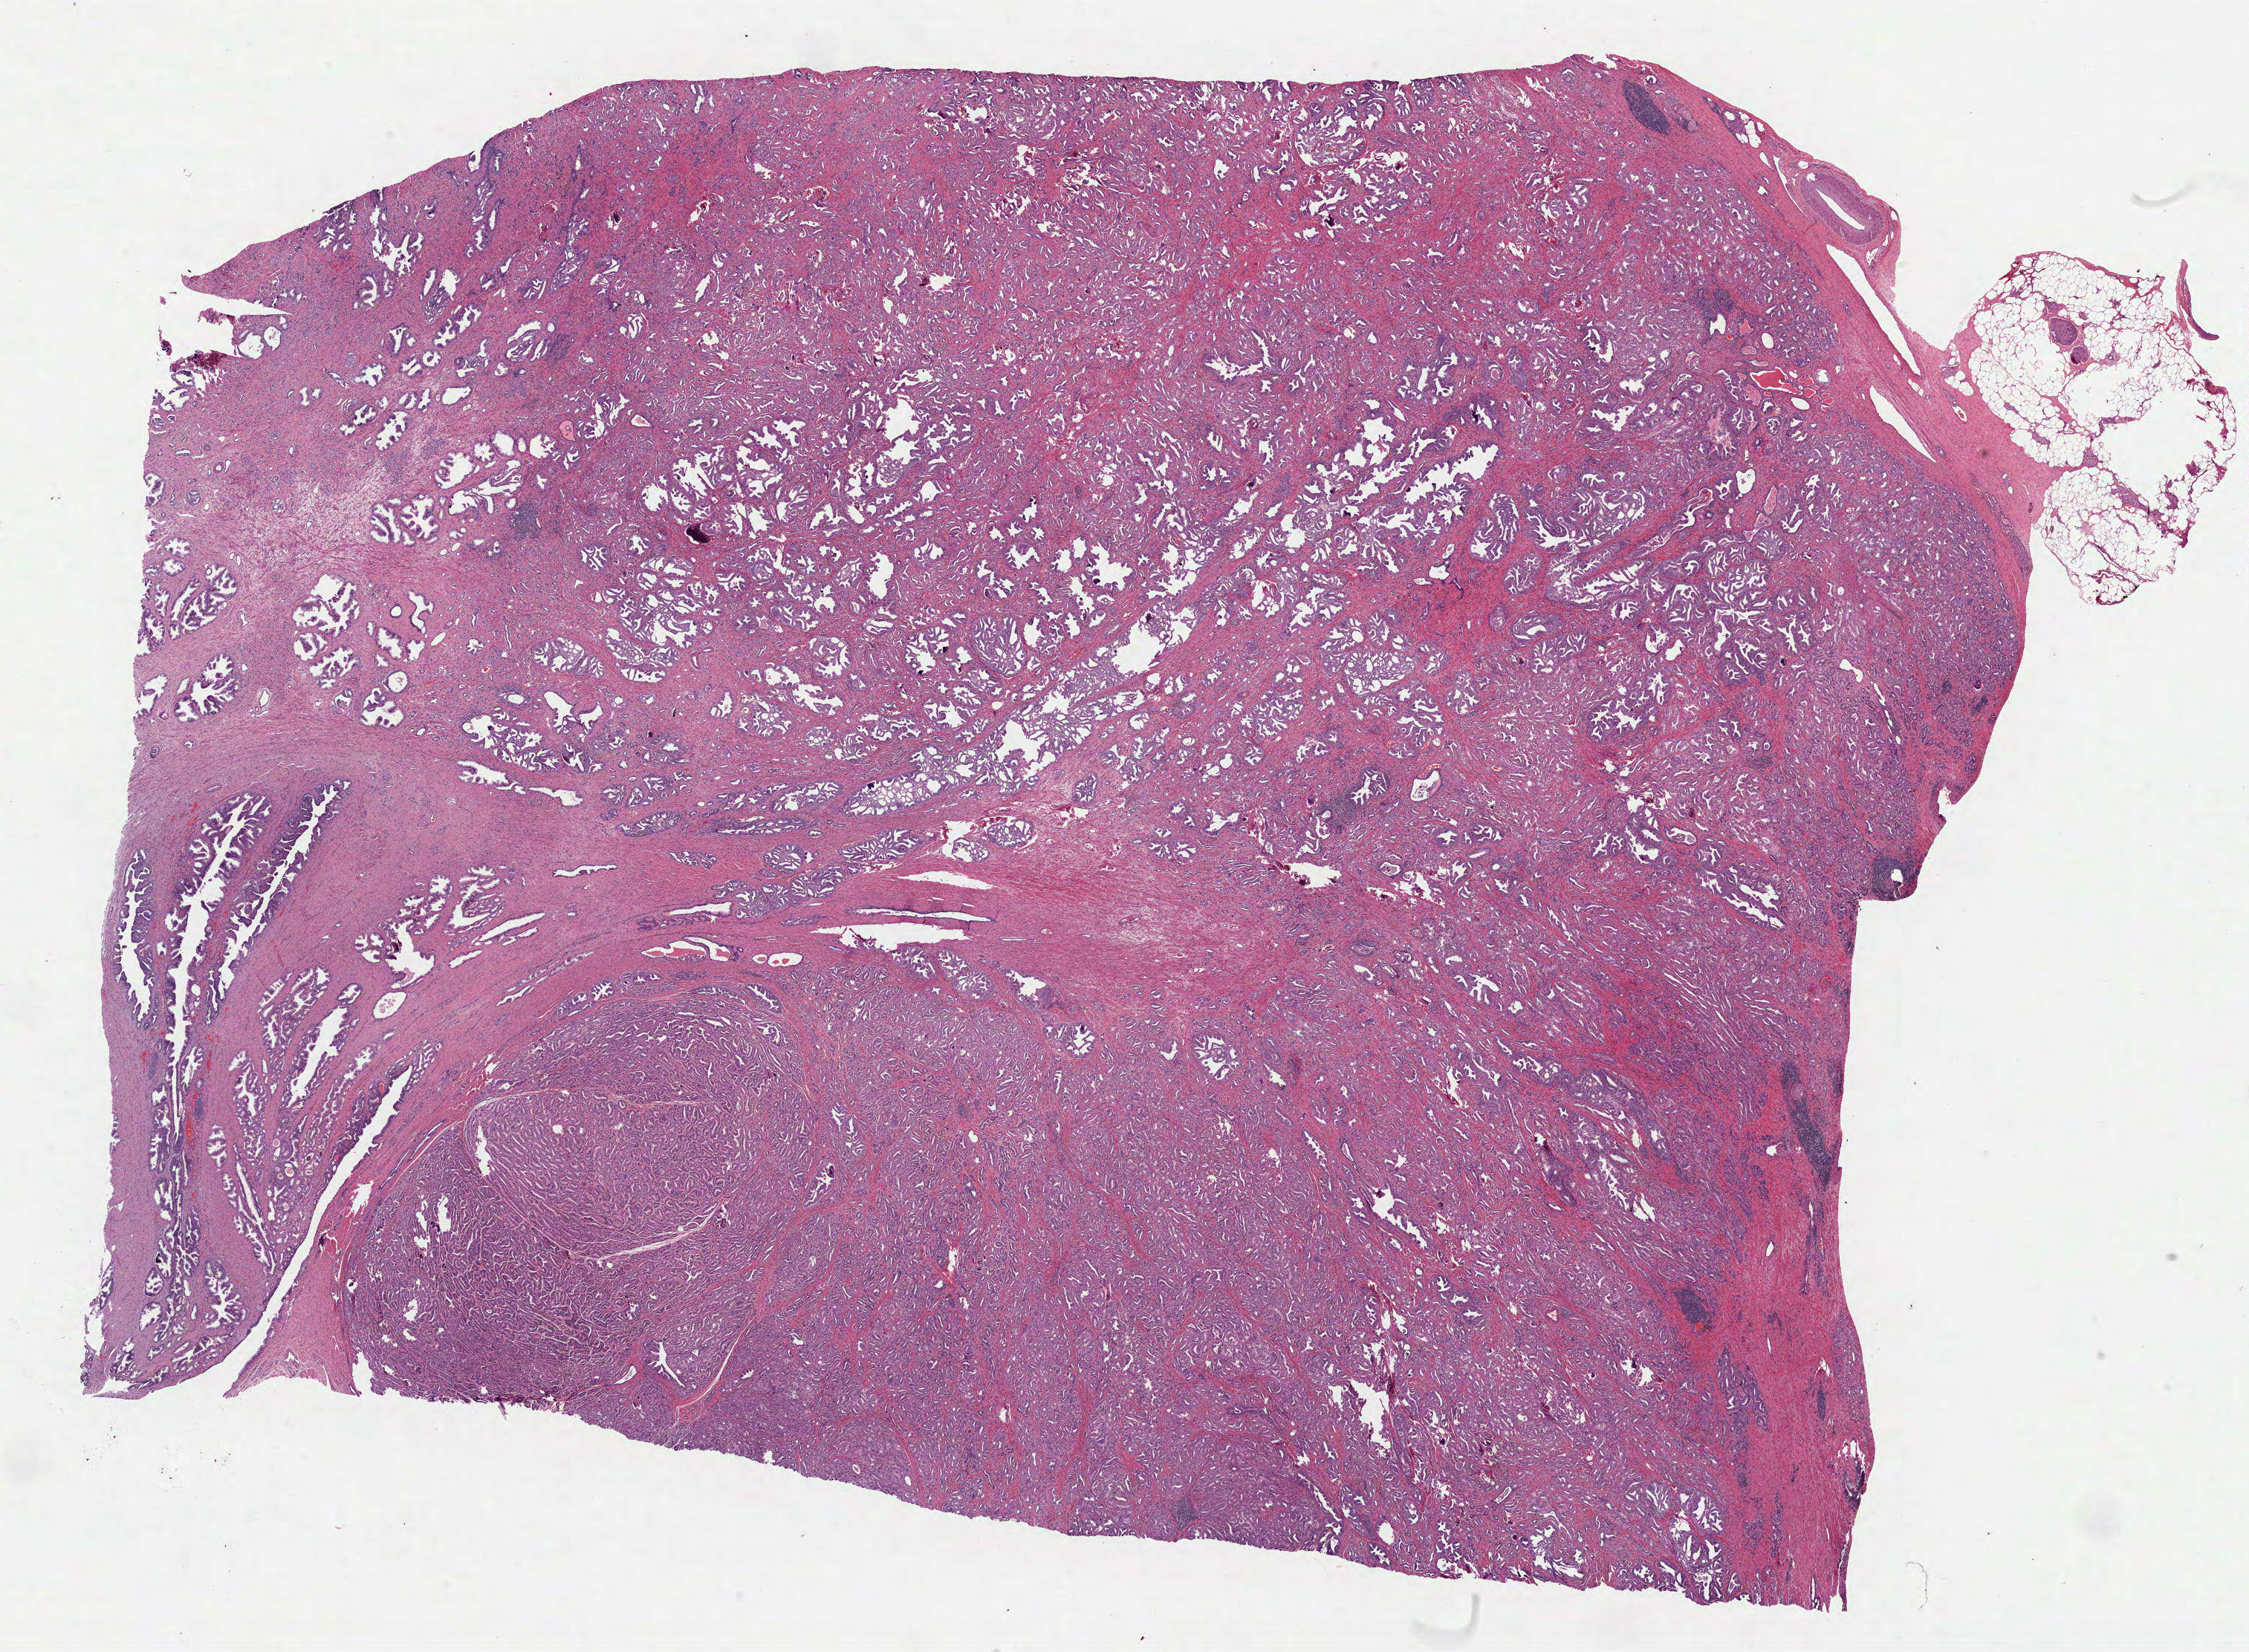
Whole-slide histology image, H&E-stained — shown as a low-resolution overview of the whole scanned area (about 24.4 x 17.9 mm, slide scanned at 40x), formalin-fixed paraffin-embedded (FFPE) diagnostic section, sample: primary tumour, prostate. Patient: male, age at initial diagnosis 53 years.
Diagnosis: Acinar cell carcinoma.